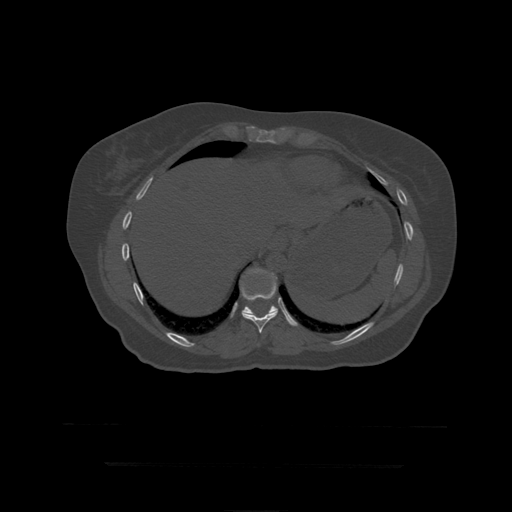
CT including the spine, one axial slice; position 235 of 399 along the scan axis; reconstruction kernel STANDARD; 120 kVp; bone window (W 1800 / L 400 HU); 512 × 512 image matrix. Patient age 41 years. Case-level facts recorded for this patient, not image findings: primary cancer: breast.
Structures marked on this image (semi-automatically segmented with operator editing):
- T10 vertebra: bounding box [x1, y1, x2, y2] px = [240, 279, 278, 334]
- T11 vertebra: [242, 268, 278, 317]